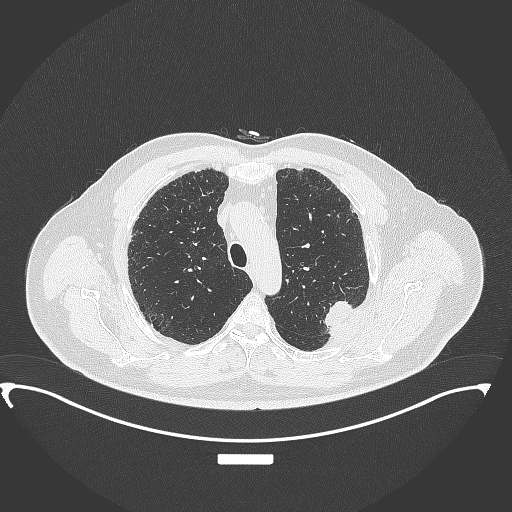
Chest CT, one axial slice. Position 275 of 350 along the scan axis. 120 kVp. Lung window (W 1500 / L -600 HU). 1 mm slice thickness. 512 × 512 image matrix, field of view 459 × 459 mm. Male patient, age 64 years. Case-level facts recorded for this patient, not image findings: clinical TNM (as recorded): T1c N1 M1.
Annotated regions visible in this slice (rectangle marked by the reading radiologist):
- lung tumour (recorded histology: adenocarcinoma): box from (x=316, y=293) to (x=356, y=338) px